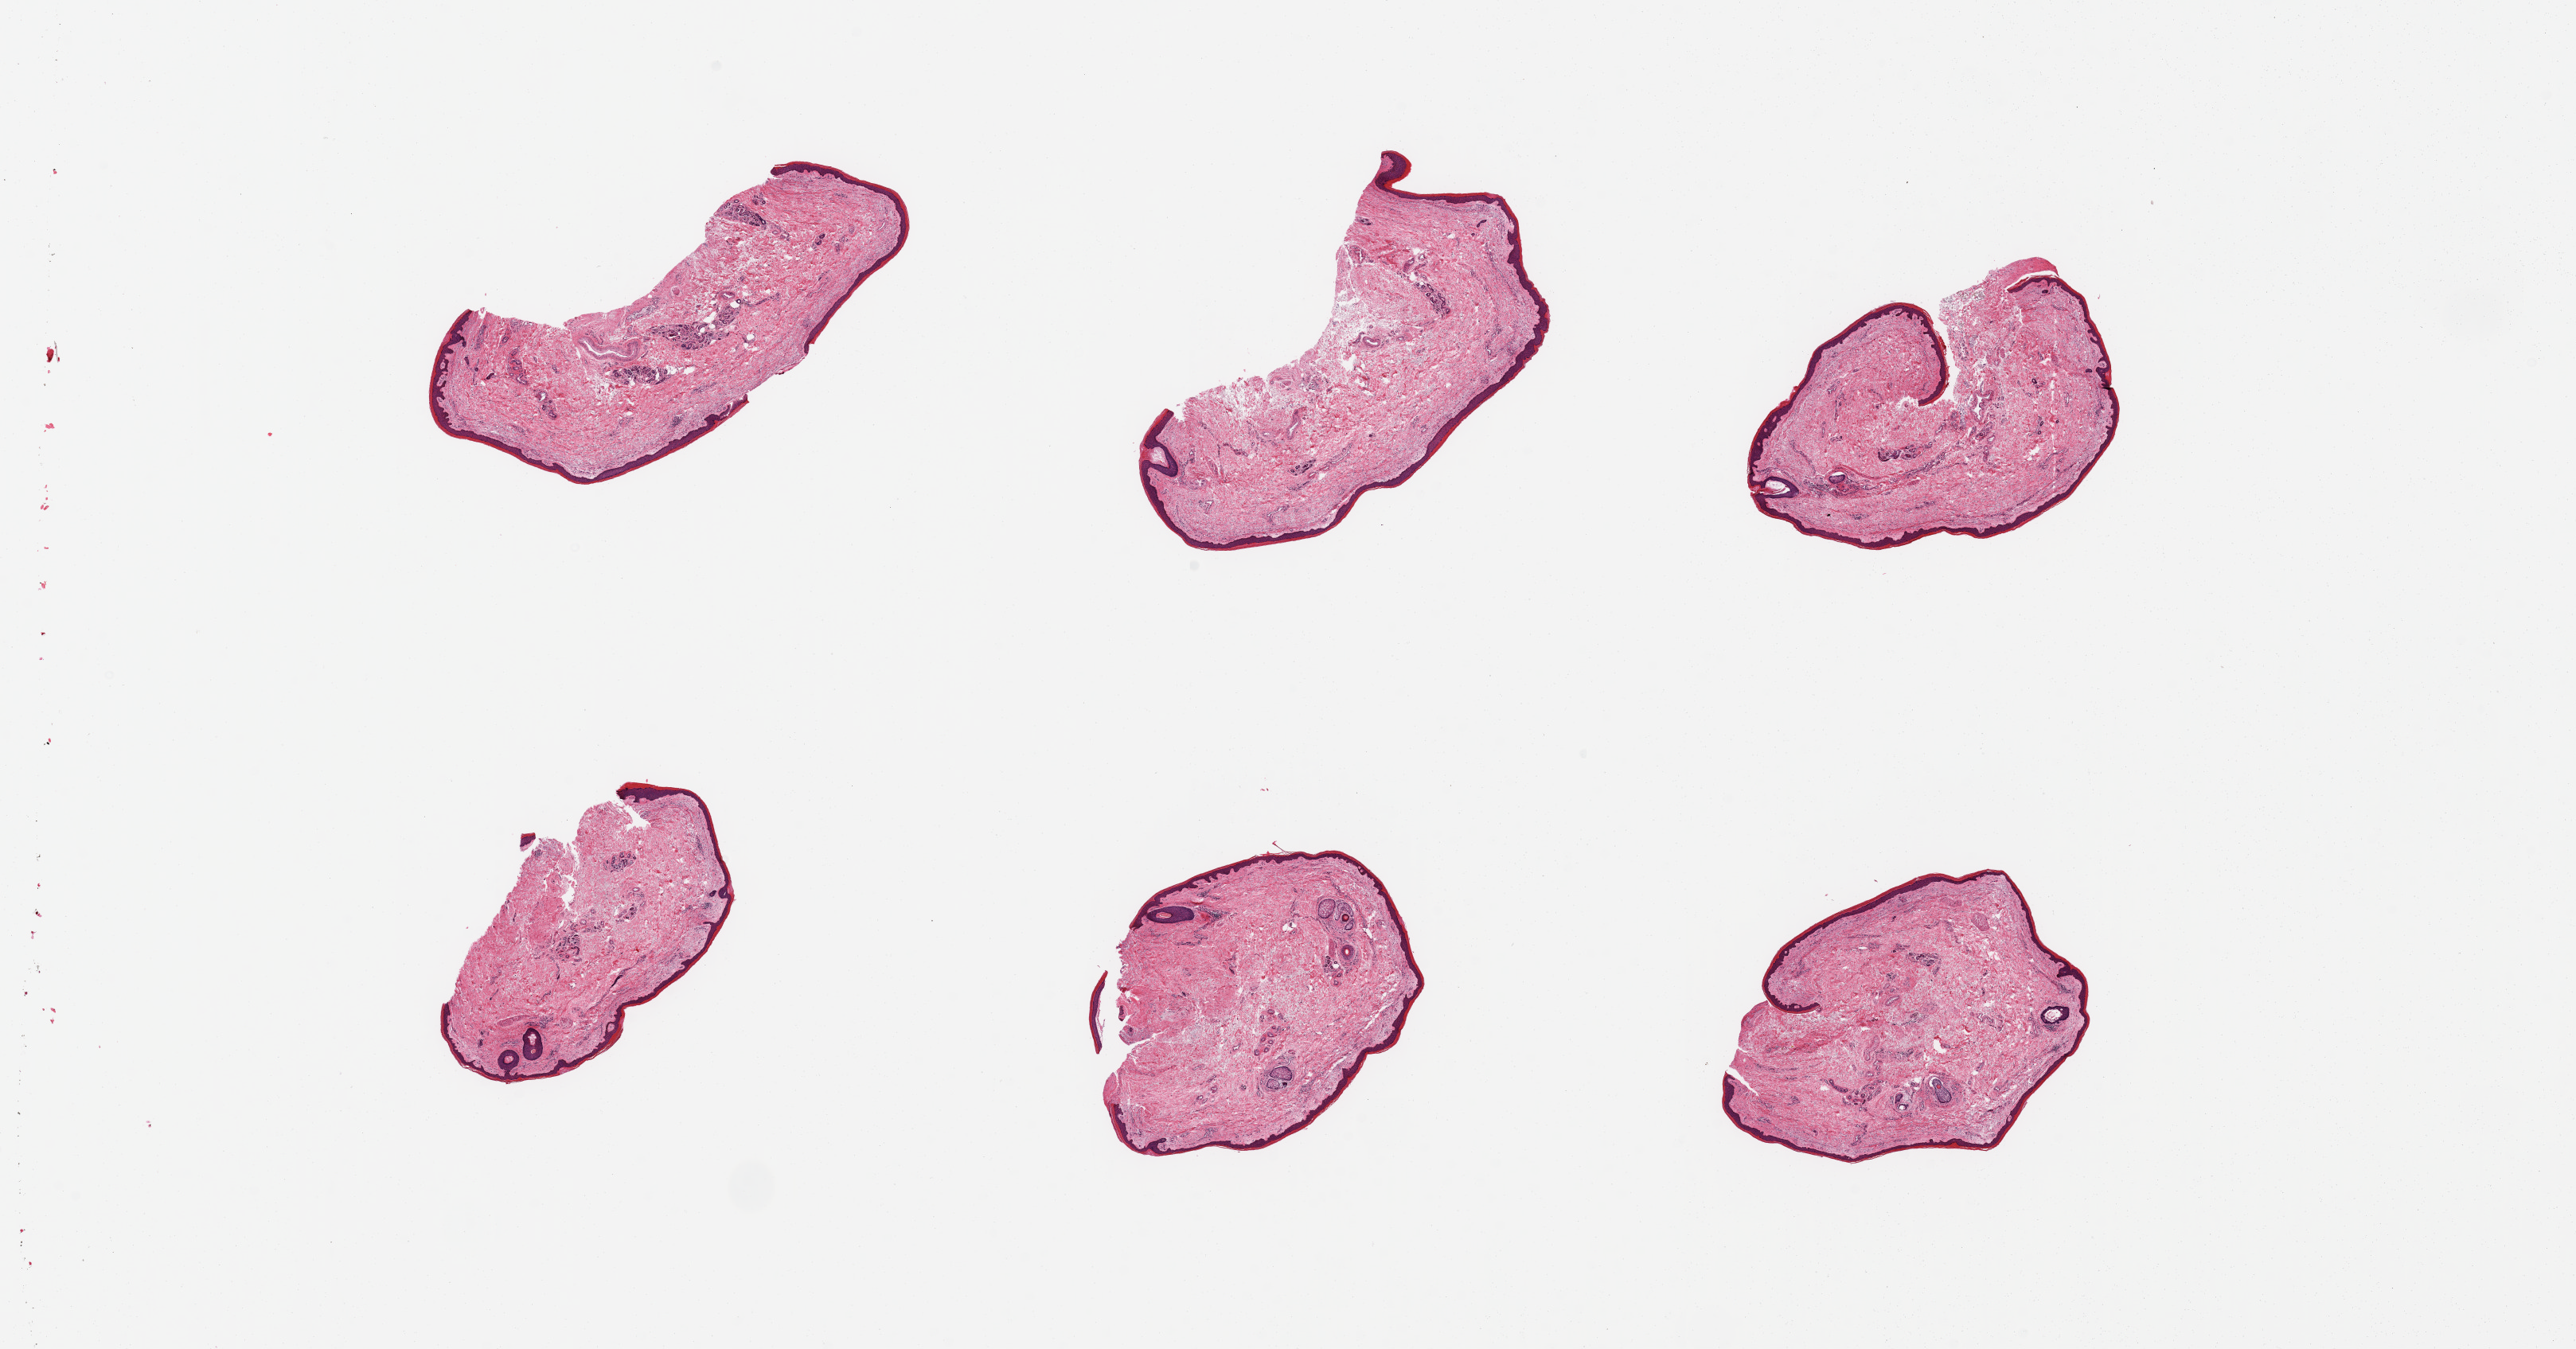
Whole-slide image, H&E stain, brightfield, low-resolution overview of the scanned area, about 25.6 x 13.4 mm (from a 20x scan), PAXgene-fixed paraffin-embedded (PFPE) section, sampled site (target tissue): skin of lower leg, donor tissue sample. Male donor.
* pathologist's review note for this sample: 6 pieces, minimal dermal fat; diffuse moderate dermal soalr elastosis; squamous epithelium is ~60 microns